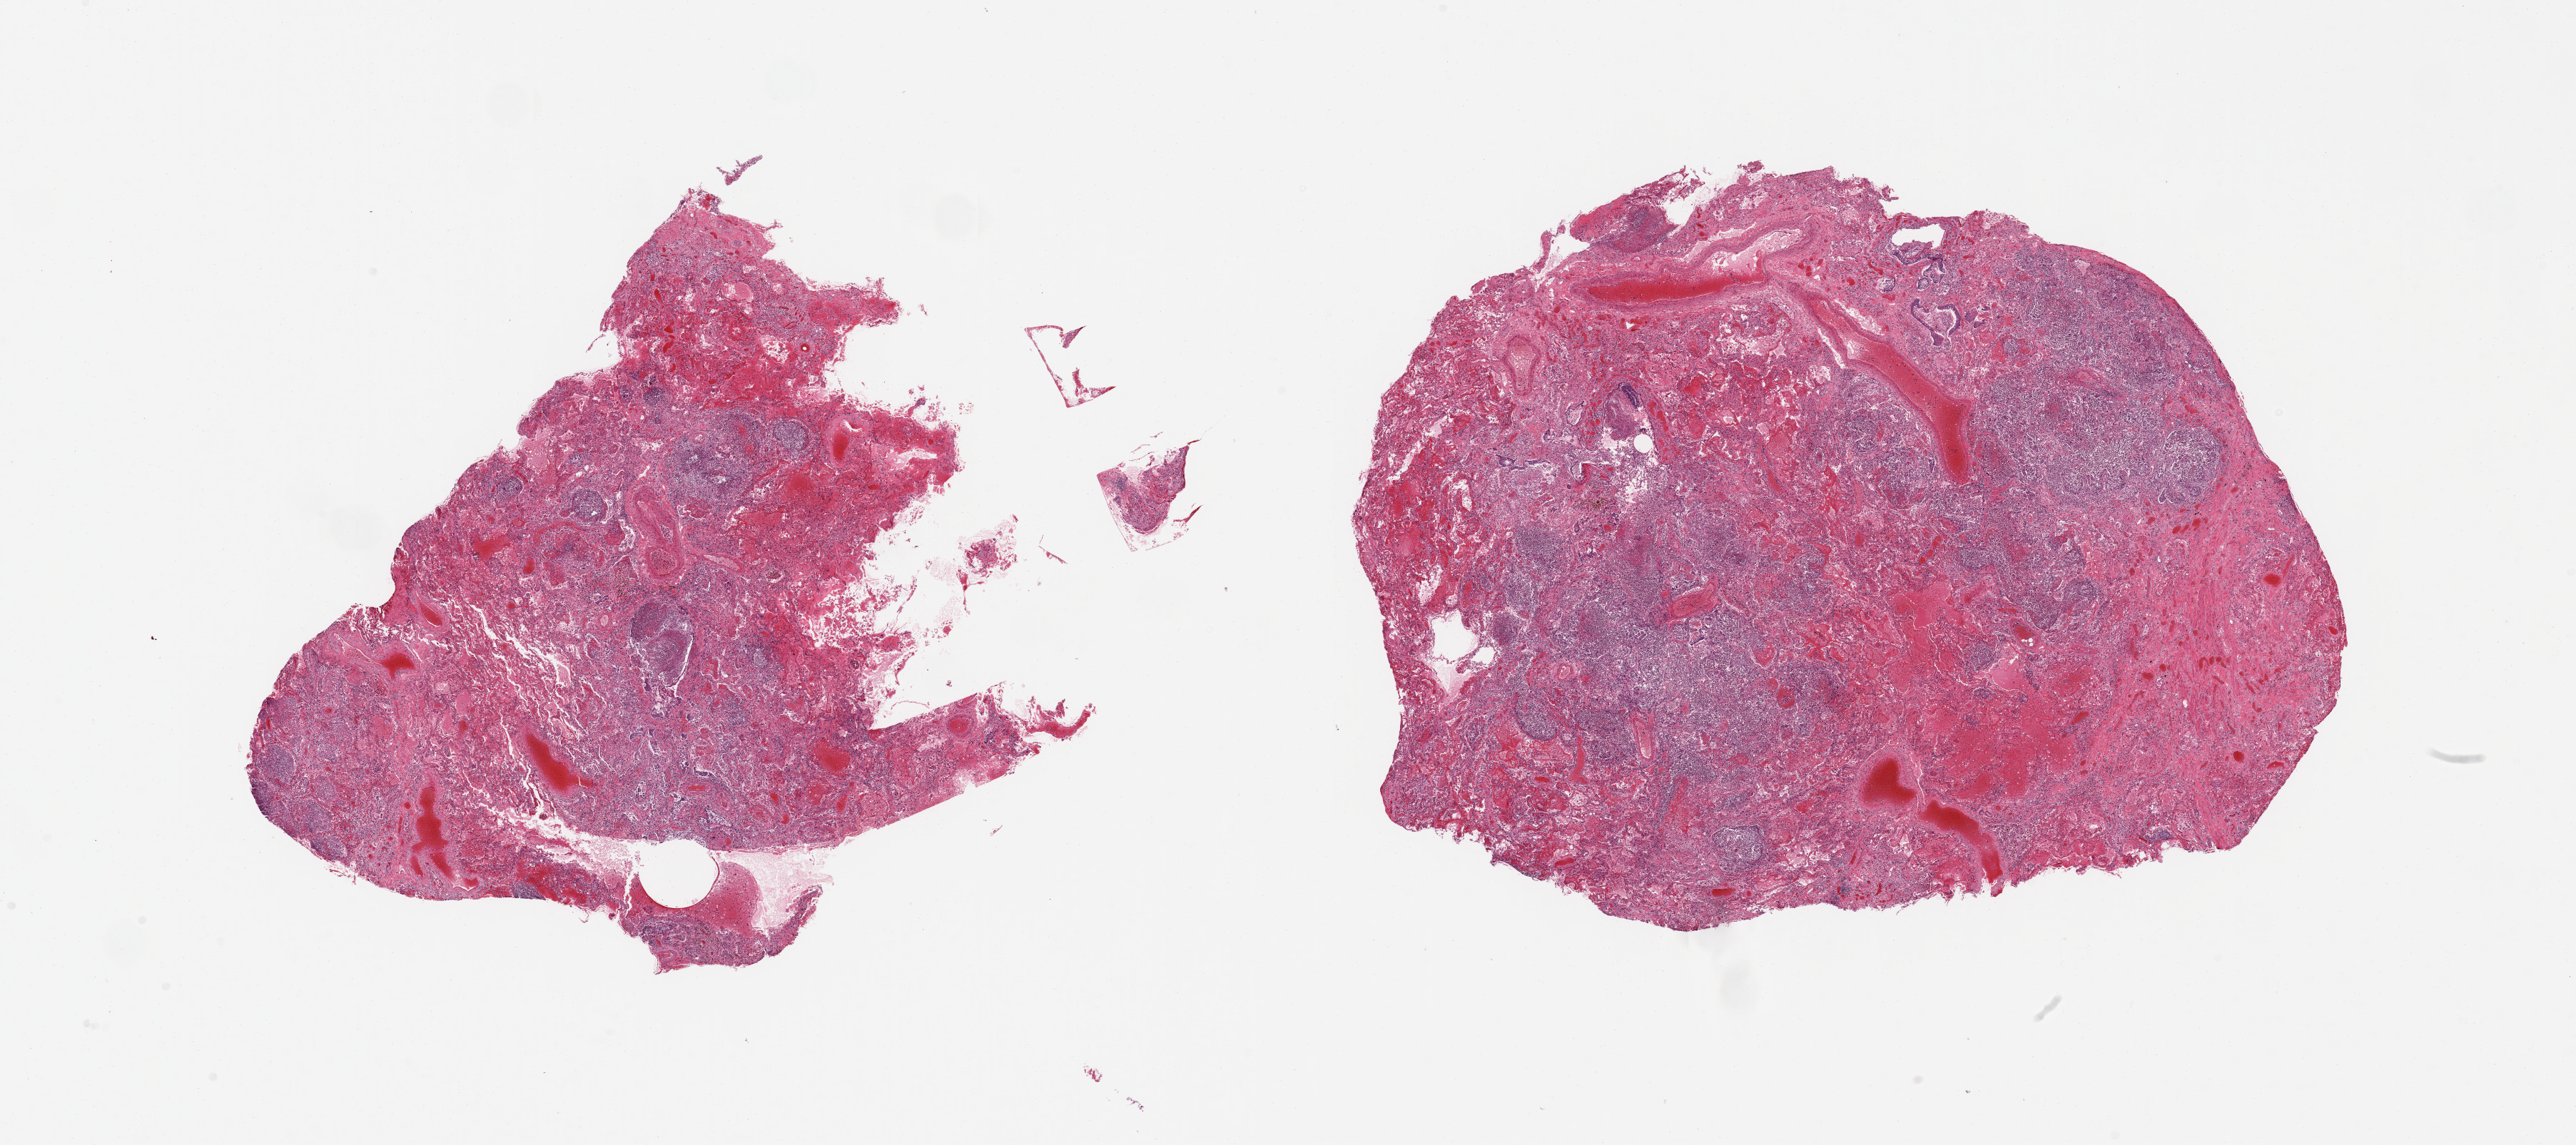
Hematoxylin and eosin (H&E) whole-slide image — low-resolution overview of the scanned area, about 28.5 x 12.7 mm, PAXgene-fixed paraffin-embedded (PFPE) section, sampled site (target tissue): lung, donor tissue sample. Donor sex: male.
• review note (as recorded): 2 pieces; widespread bronchopneumonia; no unaffected lung tissue